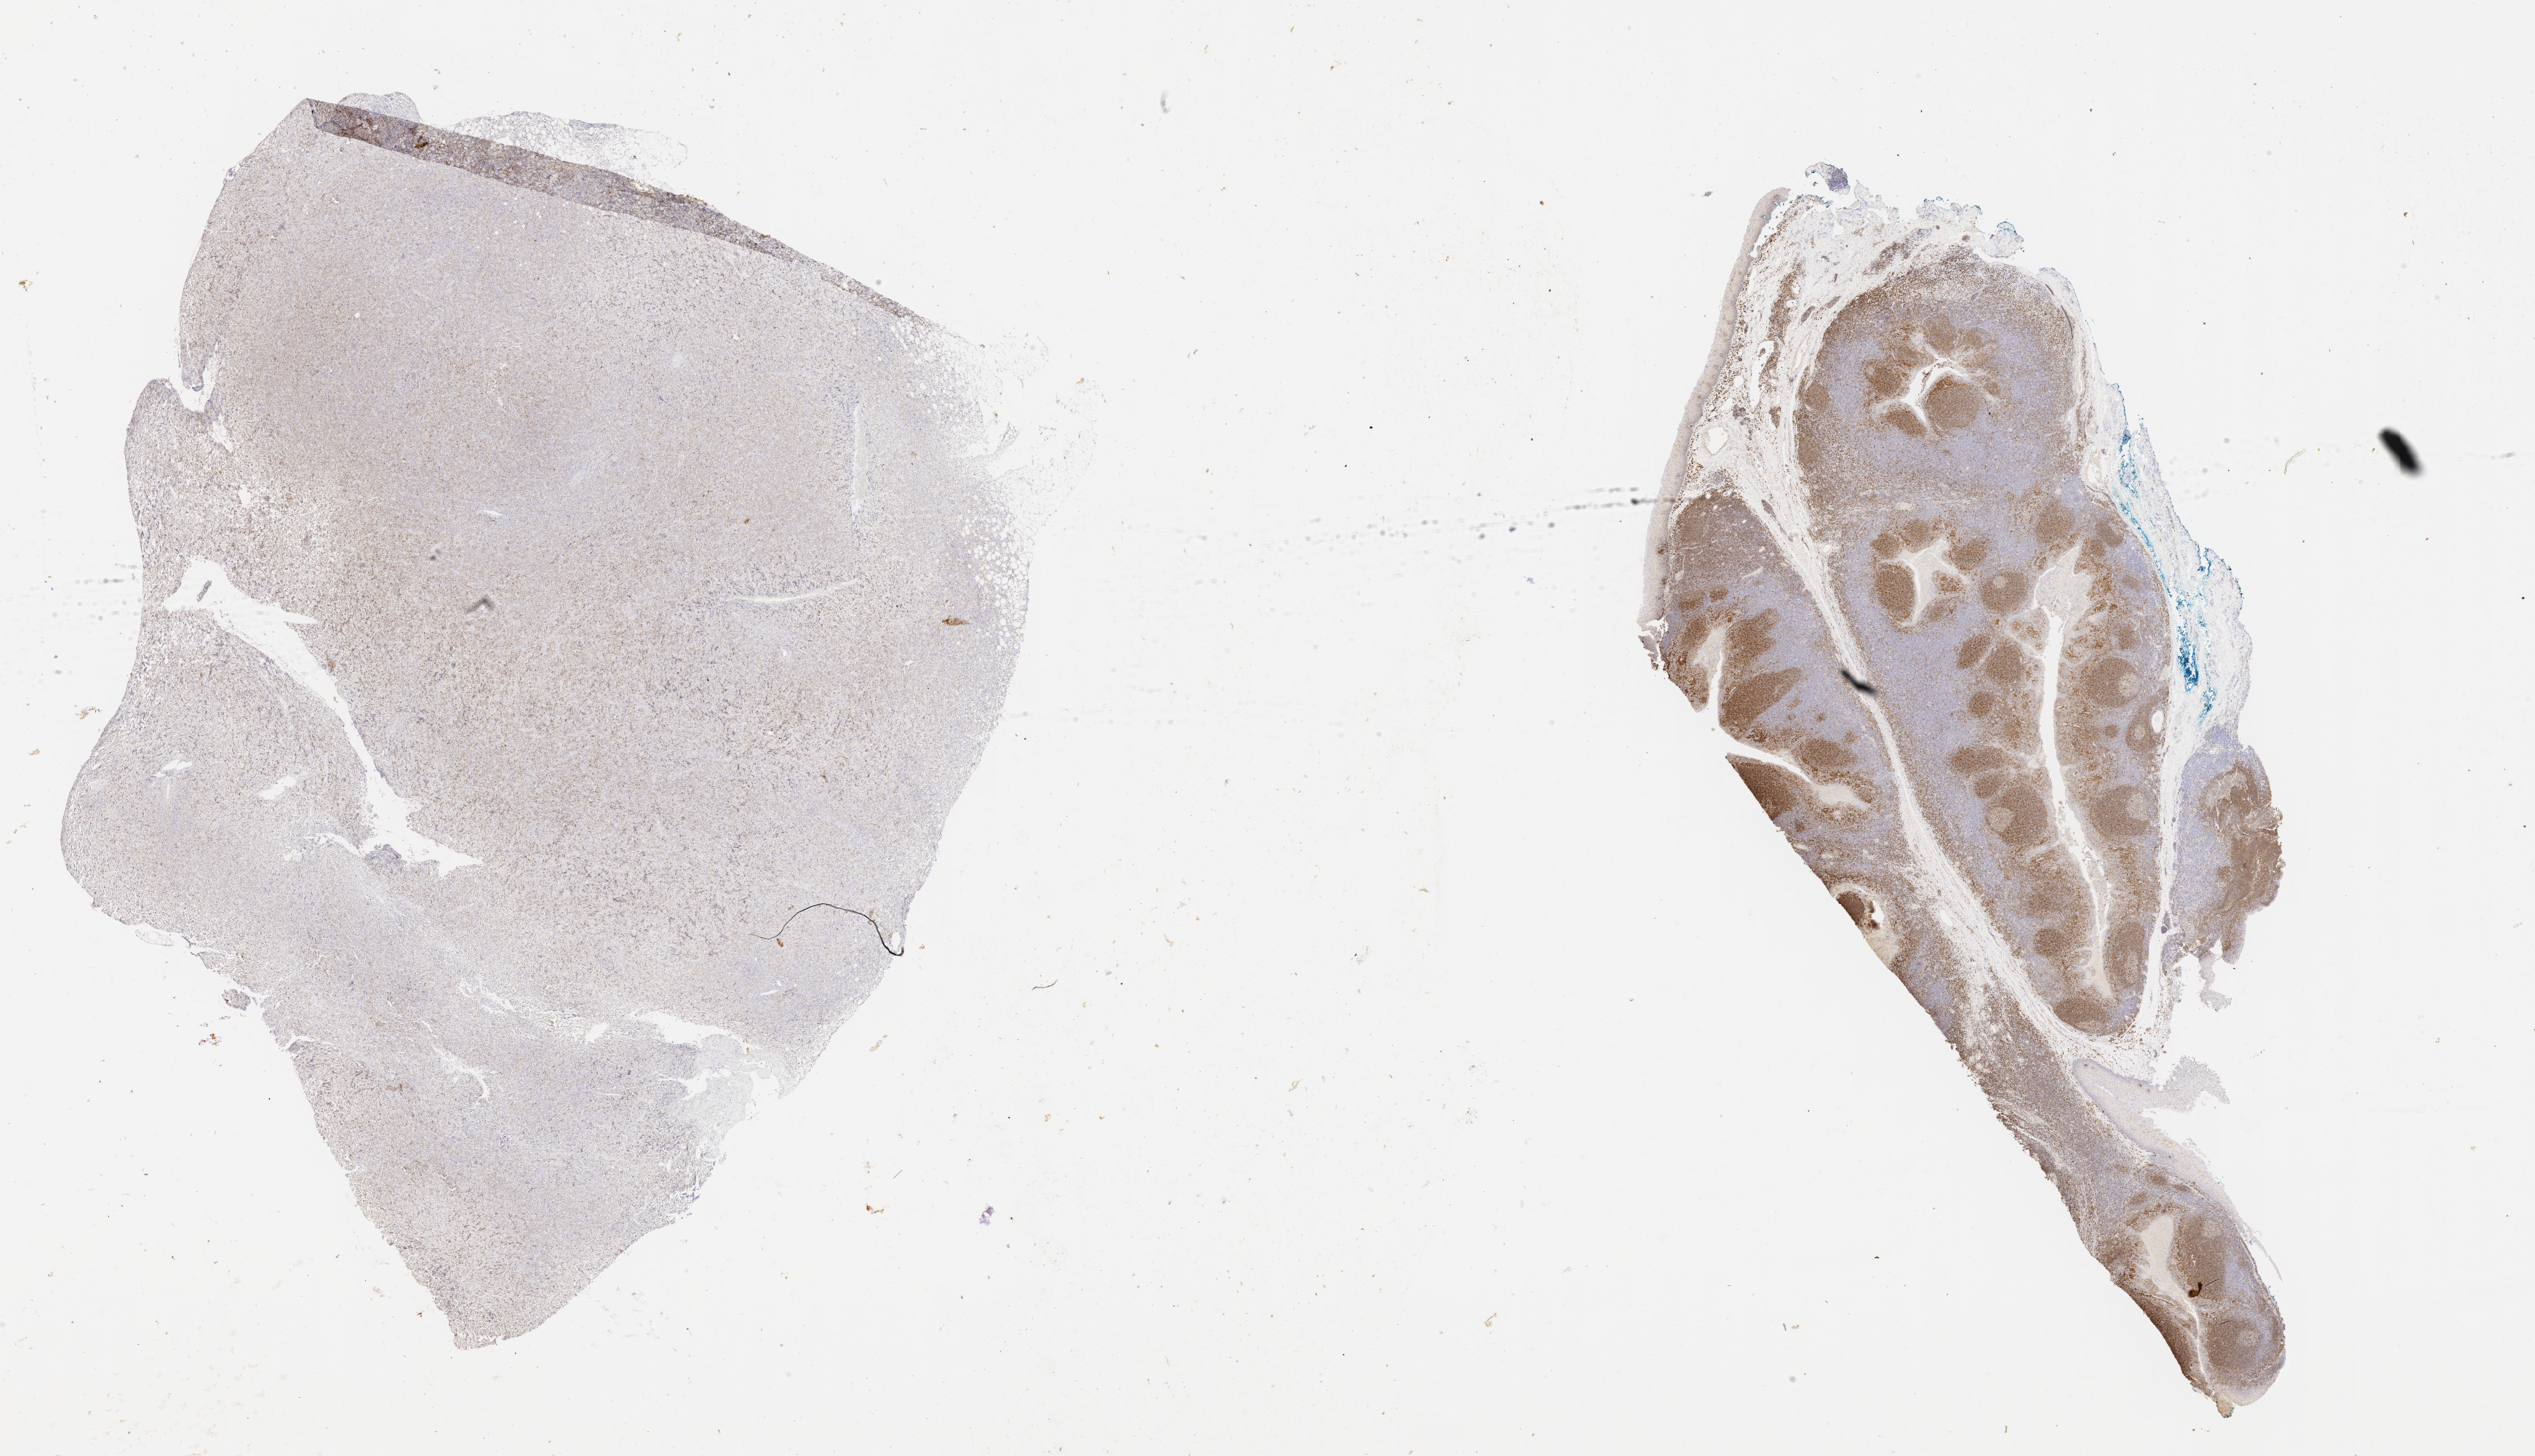
Whole-slide image, immunohistochemical stain for CD79a, low-resolution overview of the scanned area, about 28.2 x 16.2 mm. Patient sex: female.
Specimen: tumor tissue.